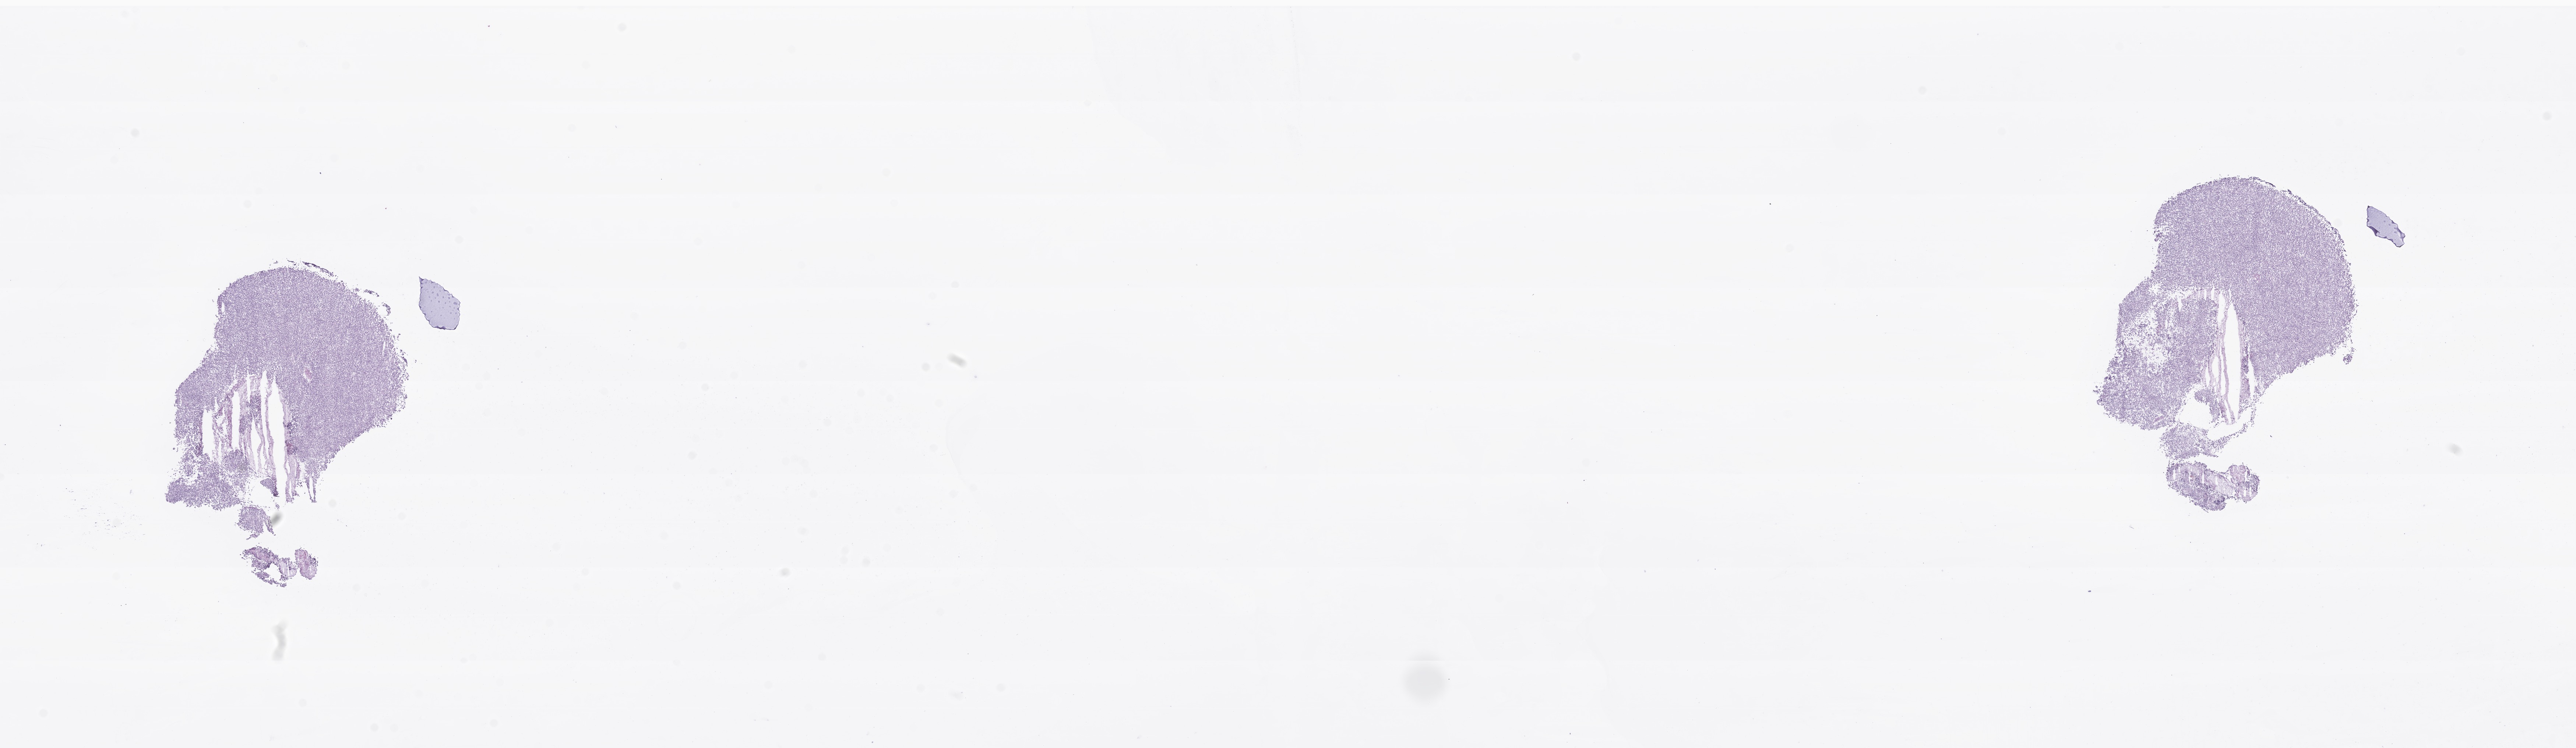
Whole-slide image, haematoxylin and eosin stain of tumor tissue from the brain — shown as a low-resolution overview of the whole scanned area (about 29.4 x 8.5 mm); frozen section (OCT-embedded). Patient female; age 78 months.
Diagnosis: Glioma, malignant.